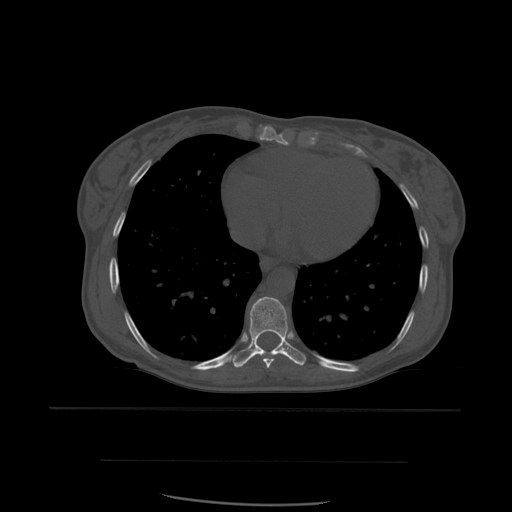
CT including the spine, one axial slice; slice 341 of 574 in the series (ordered by position); bone window (W 1800 / L 400 HU); 1.25 mm slice thickness; 512 × 512 image matrix. Patient age 48 years. From the clinical record (not read from this slice): primary cancer: lung; vertebrae with lytic lesions (as recorded): T11.
Structures marked on this image (semi-automatic segmentation, software-assisted and operator-edited):
- T8 vertebra: bounding box [x1, y1, x2, y2] px = [263, 356, 275, 369]
- T9 vertebra: [233, 297, 307, 368]